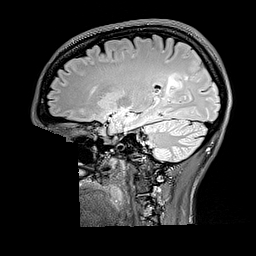
Brain MRI from a brain-tumour surgery series, one sagittal slice; slice 108 of 176 in the series (ordered by position); T2 FLAIR; 256 × 256 image matrix, field of view 256 × 256 mm. Case-level facts recorded for this patient, not image findings: histopathology: Oligodendroglioma; WHO grade: 2; IDH mutation: yes; tumour location: Right Parietal.
Outlined on this slice (manually delineated by an expert):
- tumour: box from (x=162, y=74) to (x=184, y=103) px